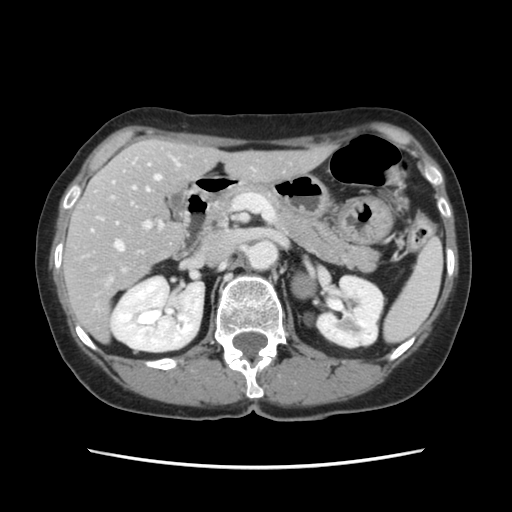
Contrast-enhanced abdominal CT, one axial slice. Position 66 of 120 along the scan axis. Intravenous contrast given. Soft-tissue window (W 400 / L 40 HU). 2.5 mm slice thickness. 512 × 512 image matrix. Female patient, age 70 years. Case-level facts recorded for this patient, not image findings: diagnosis: colorectal cancer liver metastases, imaged before liver resection; multiple liver metastases: no; largest metastasis: 2.5 cm; disease in both lobes: no.
Structures marked on this image (expert manual segmentation):
- hepatic veins: bounding box [x1, y1, x2, y2] px = [115, 165, 161, 251]
- liver: [65, 140, 326, 340]
- planned liver remnant (the part of the liver to remain after resection): [81, 140, 327, 279]
- portal vein (with intrahepatic branches): [101, 158, 253, 271]